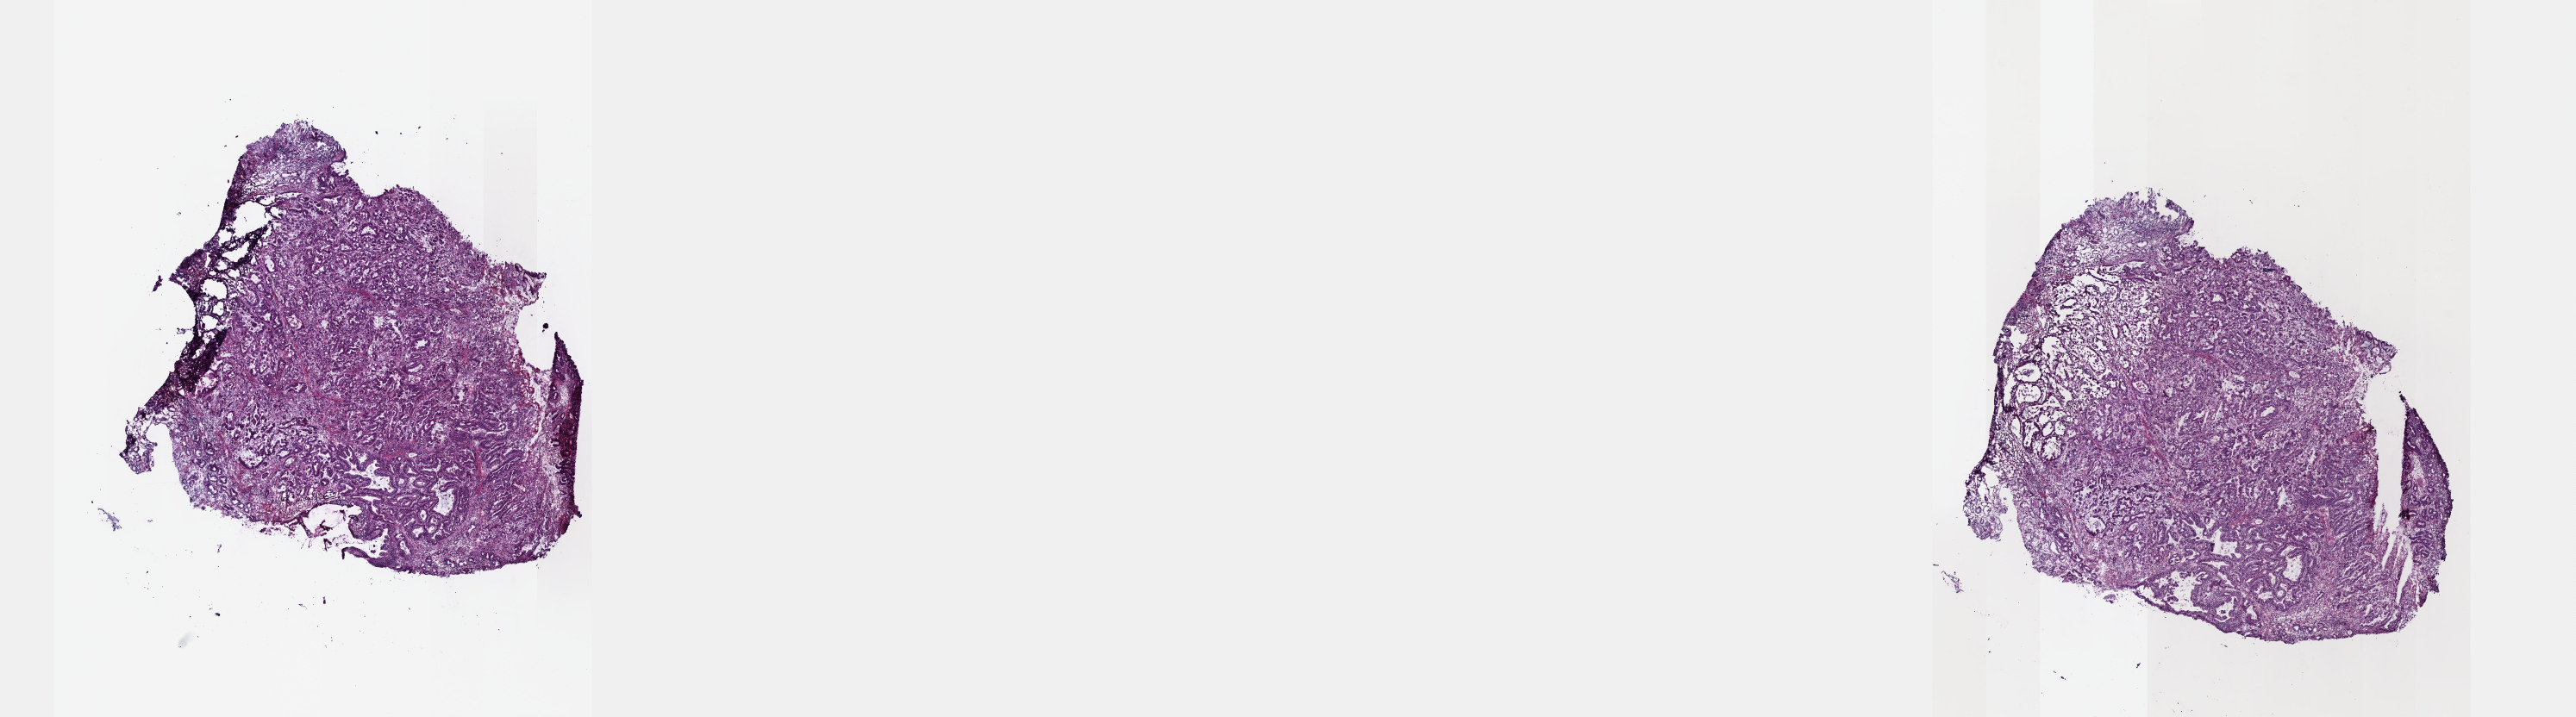
Digitized Hematoxylin and eosin (H&E) stained tissue section (whole slide) — a low-resolution overview of the entire scanned area, about 24.1 x 6.7 mm (from a 40x scan), frozen section, stomach, primary tumour sample. Female, age 52 years at initial diagnosis. Histologic grade: G2 (moderately differentiated). Slide review estimates, as recorded: tumour cells 70%, tumour nuclei 70%, normal cells 0%, stromal cells 30%, necrosis 0%. Infiltration values recorded for this section: lymphocyte infiltration 40%, monocyte infiltration 20%, neutrophil infiltration 20%.
AJCC pathologic stage: IIIC. Histologic diagnosis: Tubular adenocarcinoma (cardia, NOS).